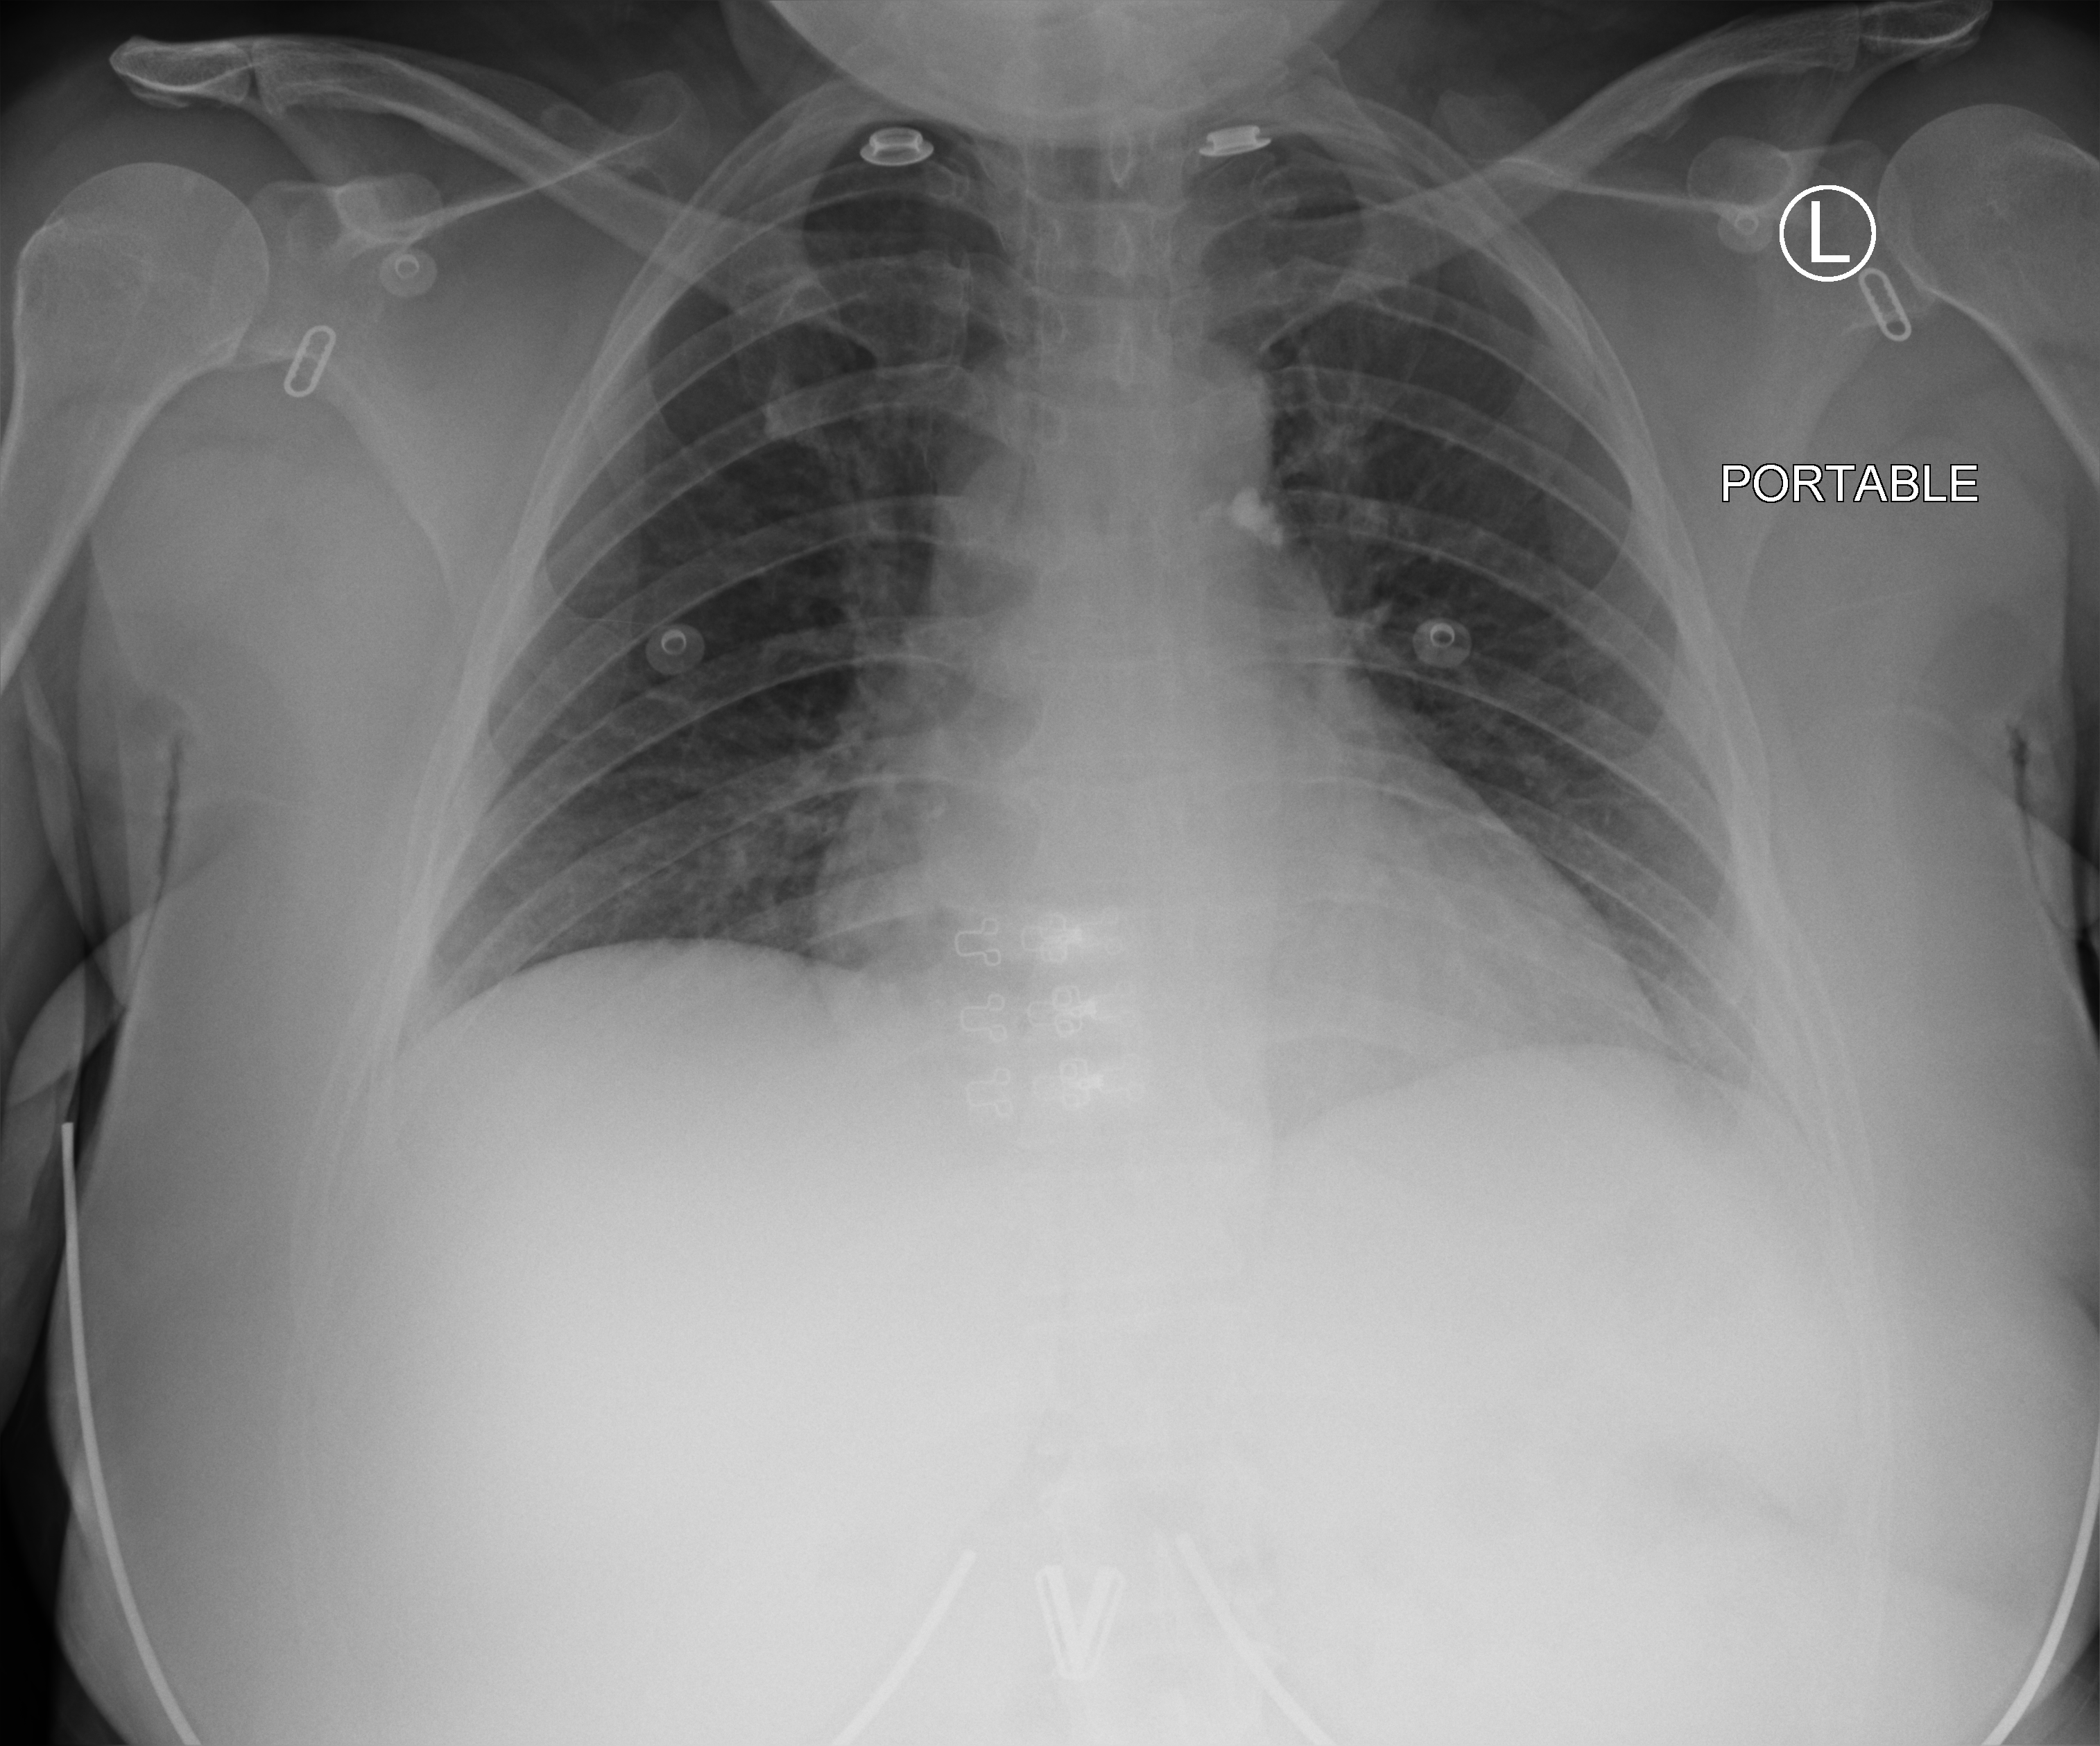
Chest X-ray (portable), anteroposterior (AP) projection. Patient hospitalised with COVID-19; female, aged 18–59 years.
From the hospital-stay record, not from the radiograph (when in the stay this image was taken is not recorded):
- length of hospital stay: 2 days
- mechanically ventilated during this hospital stay: no